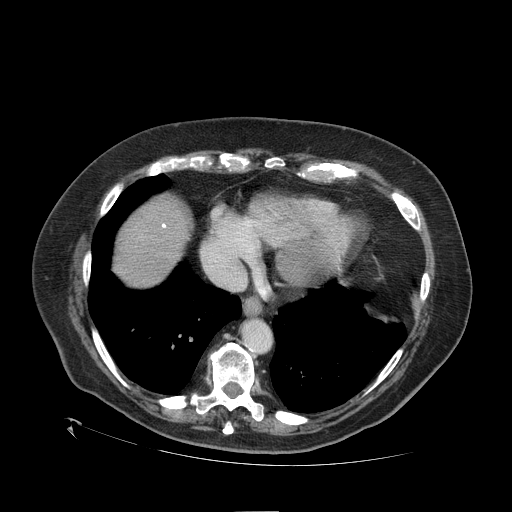
Contrast-enhanced abdominal CT (liver protocol), one axial slice. Slice 97 of 109 in the series (ordered by position). Reconstruction kernel STANDARD. 120 kVp. One of 2 acquisitions stored at this slice position. Soft-tissue window (W 400 / L 40 HU). 2.5 mm slice thickness. 512 × 512 image matrix. Case-level facts recorded for this patient, not image findings: diagnosis: hepatocellular carcinoma (patient treated with transarterial chemoembolisation; whether this scan precedes or follows treatment is not stated here); TNM stage (as recorded): Stage-I; Child-Pugh class: A; tumour differentiation: no biopsy; tumour nodularity: uninodular.
Annotated regions visible in this slice (semi-automatic segmentation, software-assisted and operator-edited):
- abdominal aorta: box from (x=243, y=319) to (x=271, y=352) px
- liver parenchyma outside the tumour (the mass and vessels are separate outlines, so this box may not span the whole liver): (x=114, y=196)–(x=192, y=286)
- liver vessels: (x=162, y=224)–(x=166, y=228)